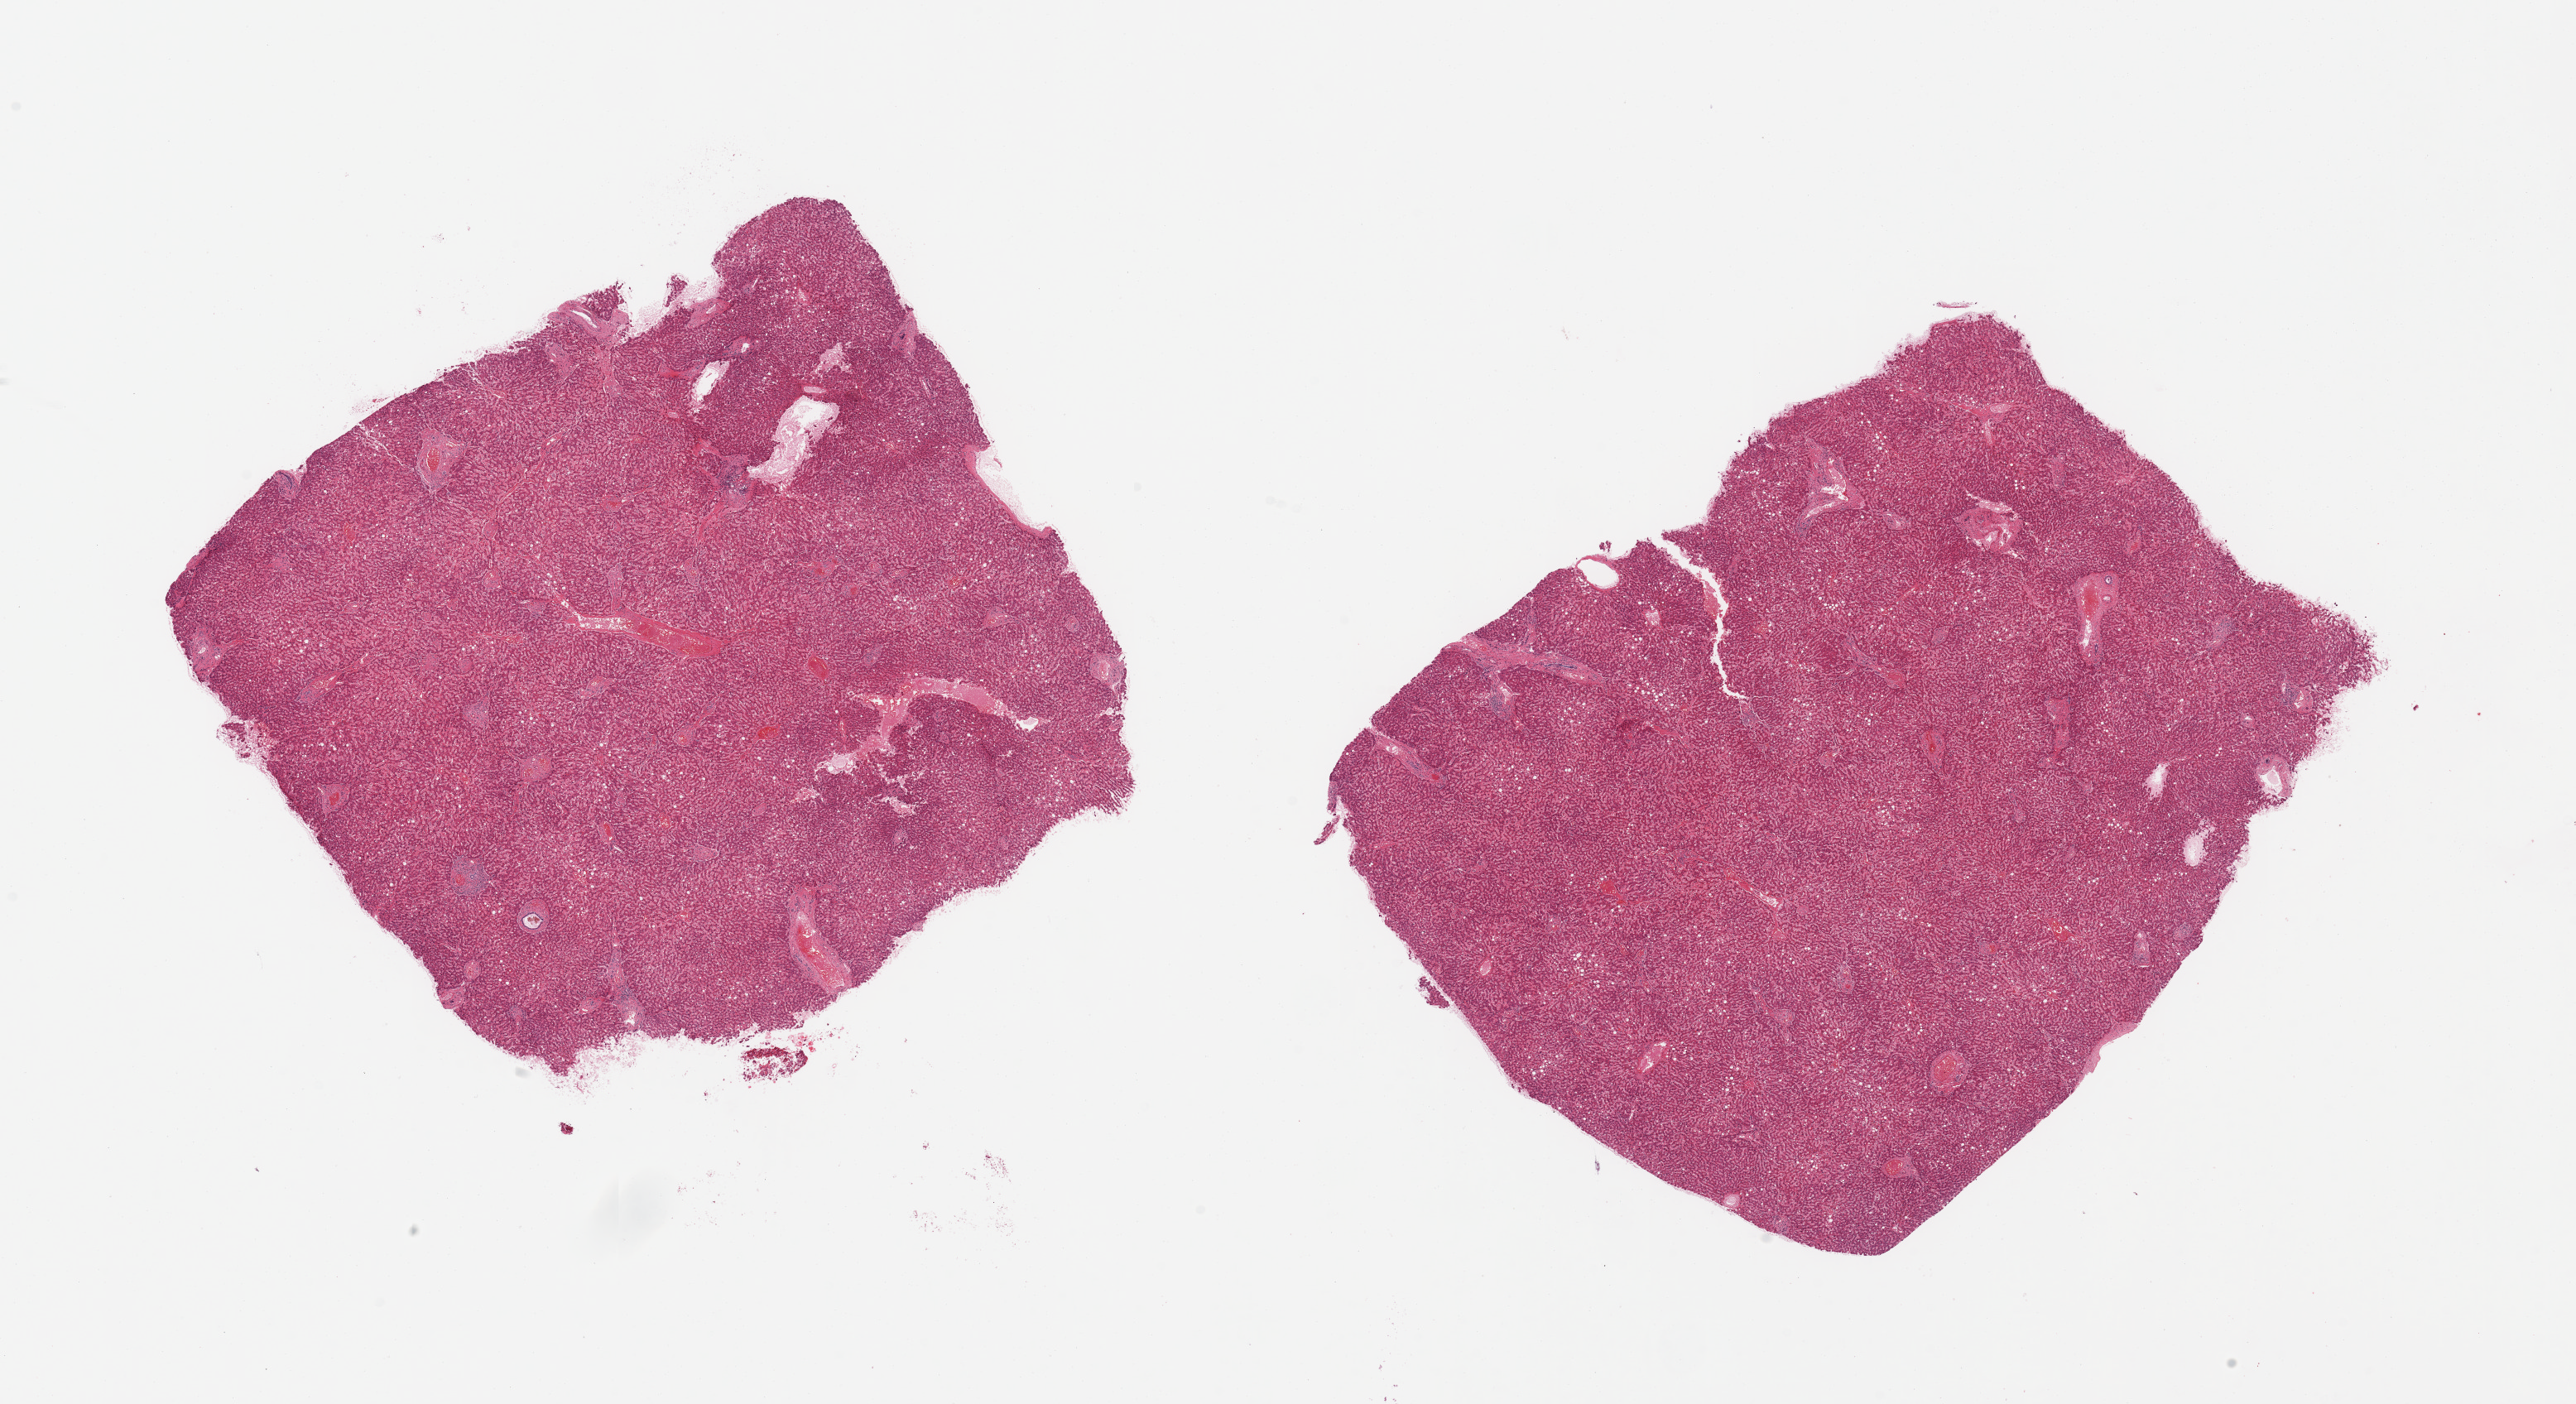
H&E whole-slide image, brightfield, whole scanned area (about 24.6 x 13.4 mm) shown as a low-resolution overview, PAXgene-fixed, paraffin-embedded tissue, section of liver (target tissue), donor tissue sample.
Reviewer comment on this tissue sample: 2 pieces, ~60-70% micro (predominately)/macrovesicular steatosis, mild chronic hepatitis.